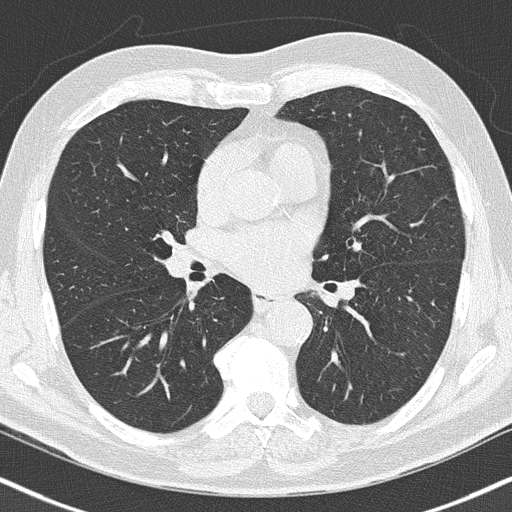
Axial slice from a low-dose chest CT screening exam, baseline annual screen, lung window (W 1500 / L -600 HU), 120 kVp, slice 90 of 186 in the series, 512 × 512 image matrix, field of view 324 × 324 mm. Male, age 66 years at enrolment. Current smoker at enrolment.
• Expert reader's lesion annotation, box from (x=185, y=273) to (x=205, y=296) px.
• Screening reader's record for this exam (one nodule recorded; not confirmed to be the boxed lesion): non-calcified nodule or mass ≥4 mm, right upper lobe, 5 × 4 mm, smooth margins.
• Later outcome: lung cancer diagnosed 778 days after this screen — squamous cell carcinoma, NOS, right lower lobe, poorly differentiated (G3), stage IIA (AJCC 6th edition), 22 mm at pathology.